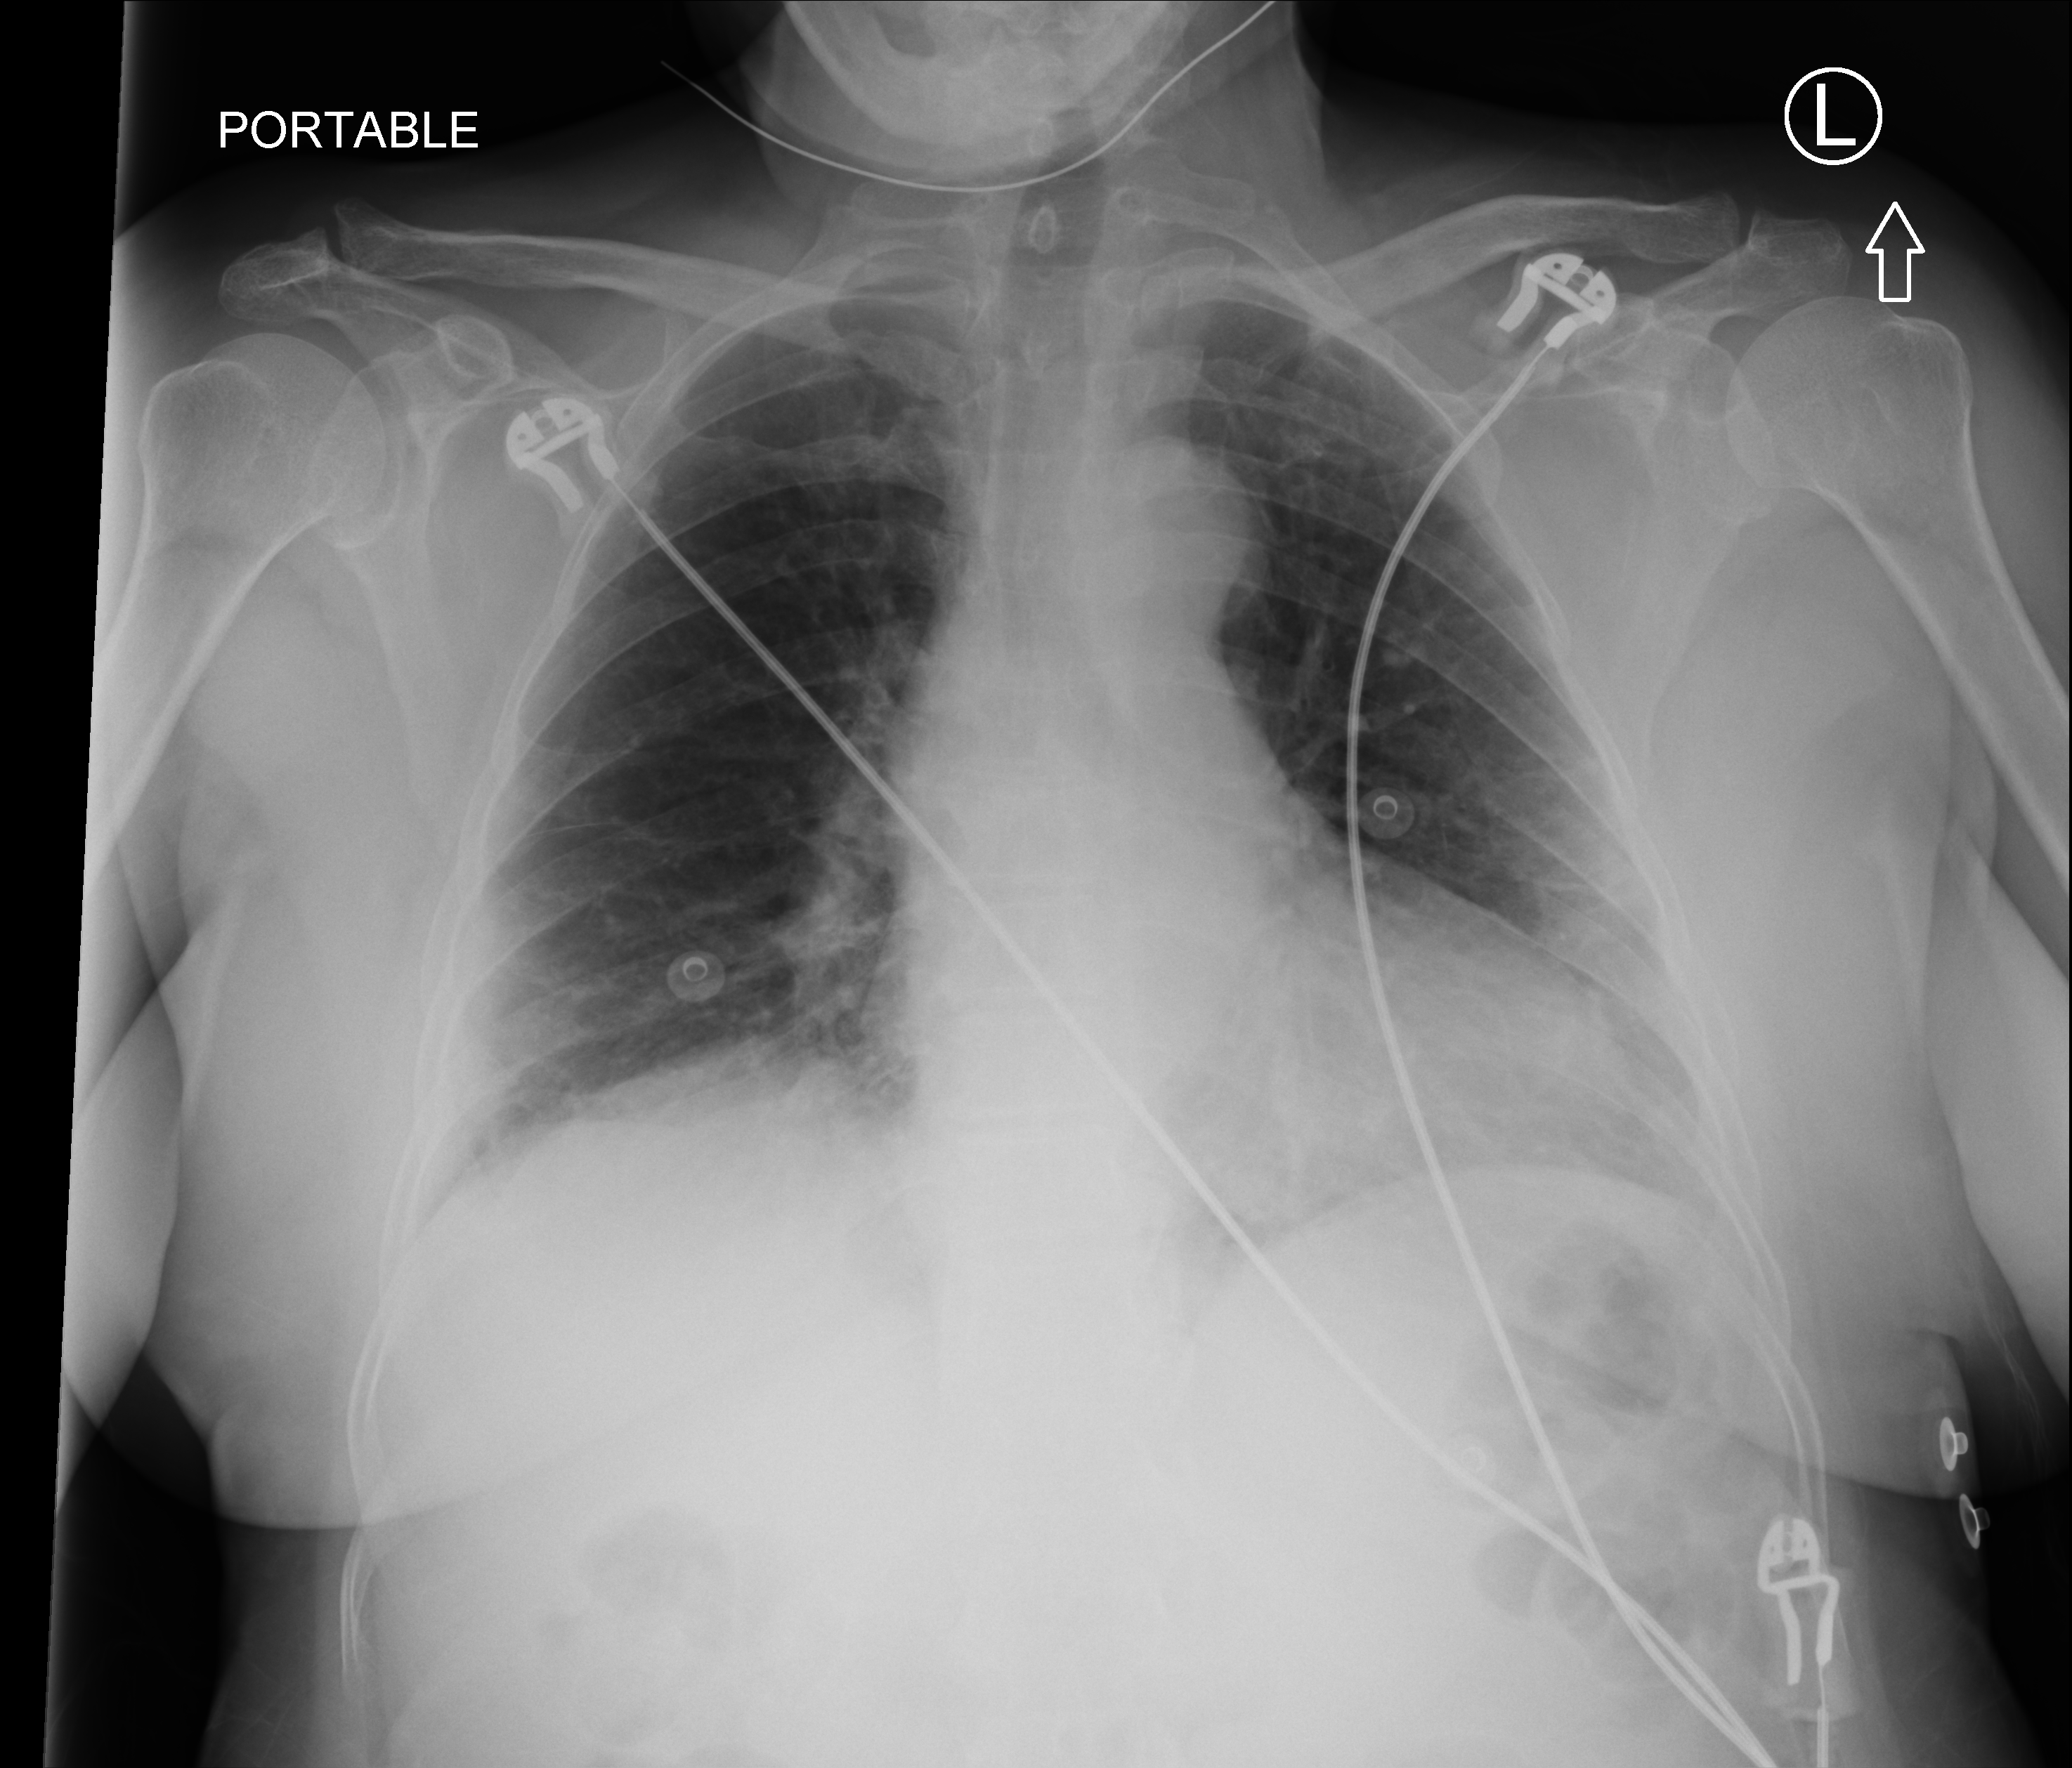
Portable chest radiograph; anteroposterior (AP) projection. Female patient hospitalised with COVID-19, age 60–74 years.
Hospital-stay facts (about this admission, not read from this image; timing relative to this image not recorded): mechanically ventilated during this hospital stay: no; admitted to intensive care during this hospital stay: no.